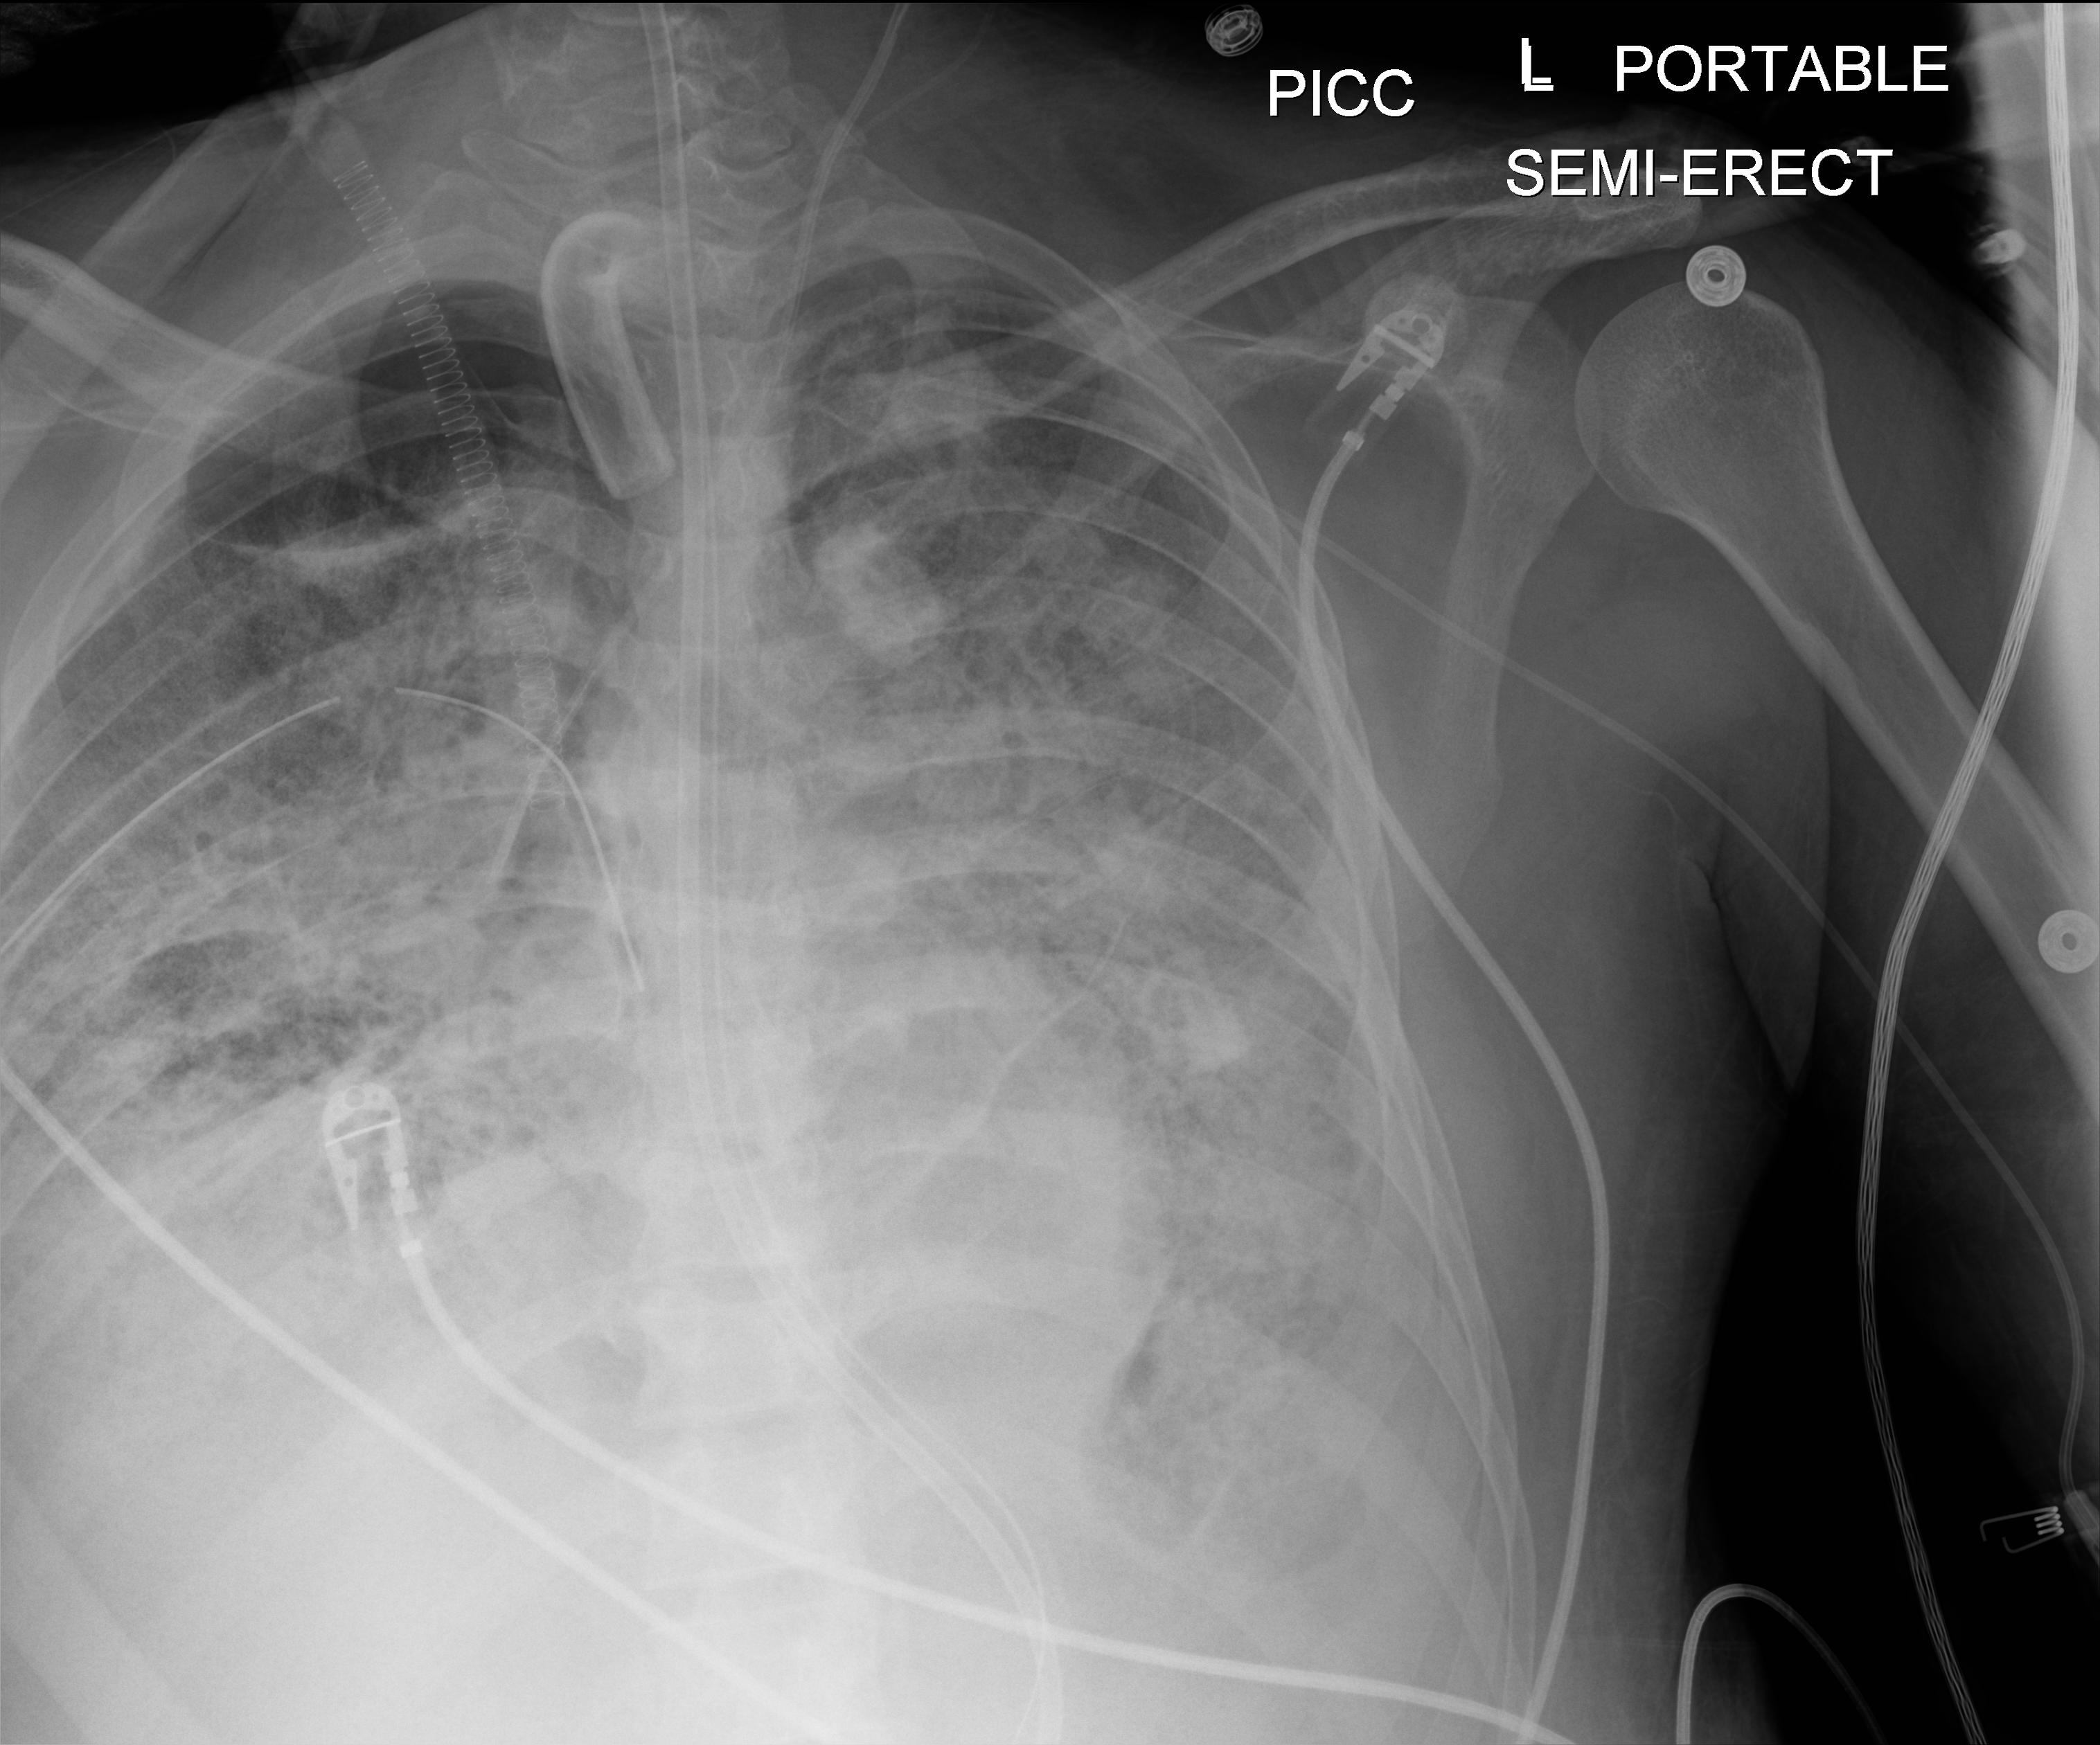
Portable chest radiograph, anteroposterior (AP) projection. Adult patient hospitalised with COVID-19, age 18–59 years.
Admission-level facts for this patient (not findings on this image; timing relative to this image not recorded): other chronic lung disease (admission record): no; mechanically ventilated during this hospital stay: yes; diabetes (admission record): no.